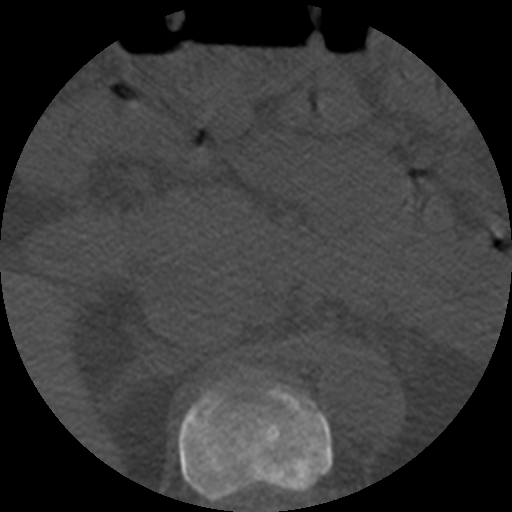
CT including the spine, one axial slice. Position 232 of 508 along the scan axis. Reconstruction kernel STANDARD. Bone window (W 1800 / L 400 HU). 1.25 mm slice thickness. 512 × 512 image matrix, field of view 160 × 160 mm. Patient age 57 years. Case-level facts recorded for this patient, not image findings: primary cancer: prostate.
Annotated regions visible in this slice (semi-automatic segmentation, software-assisted and operator-edited):
- T11 vertebra: bounding box <179,373,332,503> (left, top, right, bottom; pixels)